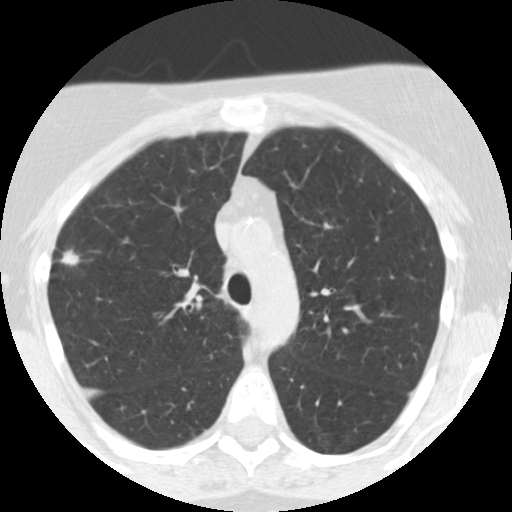
Chest CT (low-dose screening protocol), one axial image. Third annual screen. Lung window (W 1500 / L -600 HU). 2.5 mm slice thickness. Standard (soft-tissue) reconstruction kernel (STANDARD). Female participant, aged 55 years at enrolment. Current smoker at enrolment.
Expert reader's lesion annotation, bounding box (x1, y1, x2, y2) in pixels: (46, 242, 90, 281). Reader record for this screening exam (exam-level; its link to the box is not recorded): non-calcified nodule or mass ≥4 mm, right upper lobe, 10 × 10 mm, poorly defined margins, soft tissue attenuation, pre-existing on the prior screen: yes; interval growth: yes. Official screen result: positive, other. Lung cancer was diagnosed 145 days after this screen: bronchiolo-alveolar adenocarcinoma, NOS, right upper lobe, moderately differentiated (G2), stage IIA (AJCC 6th edition), 13 mm at pathology.